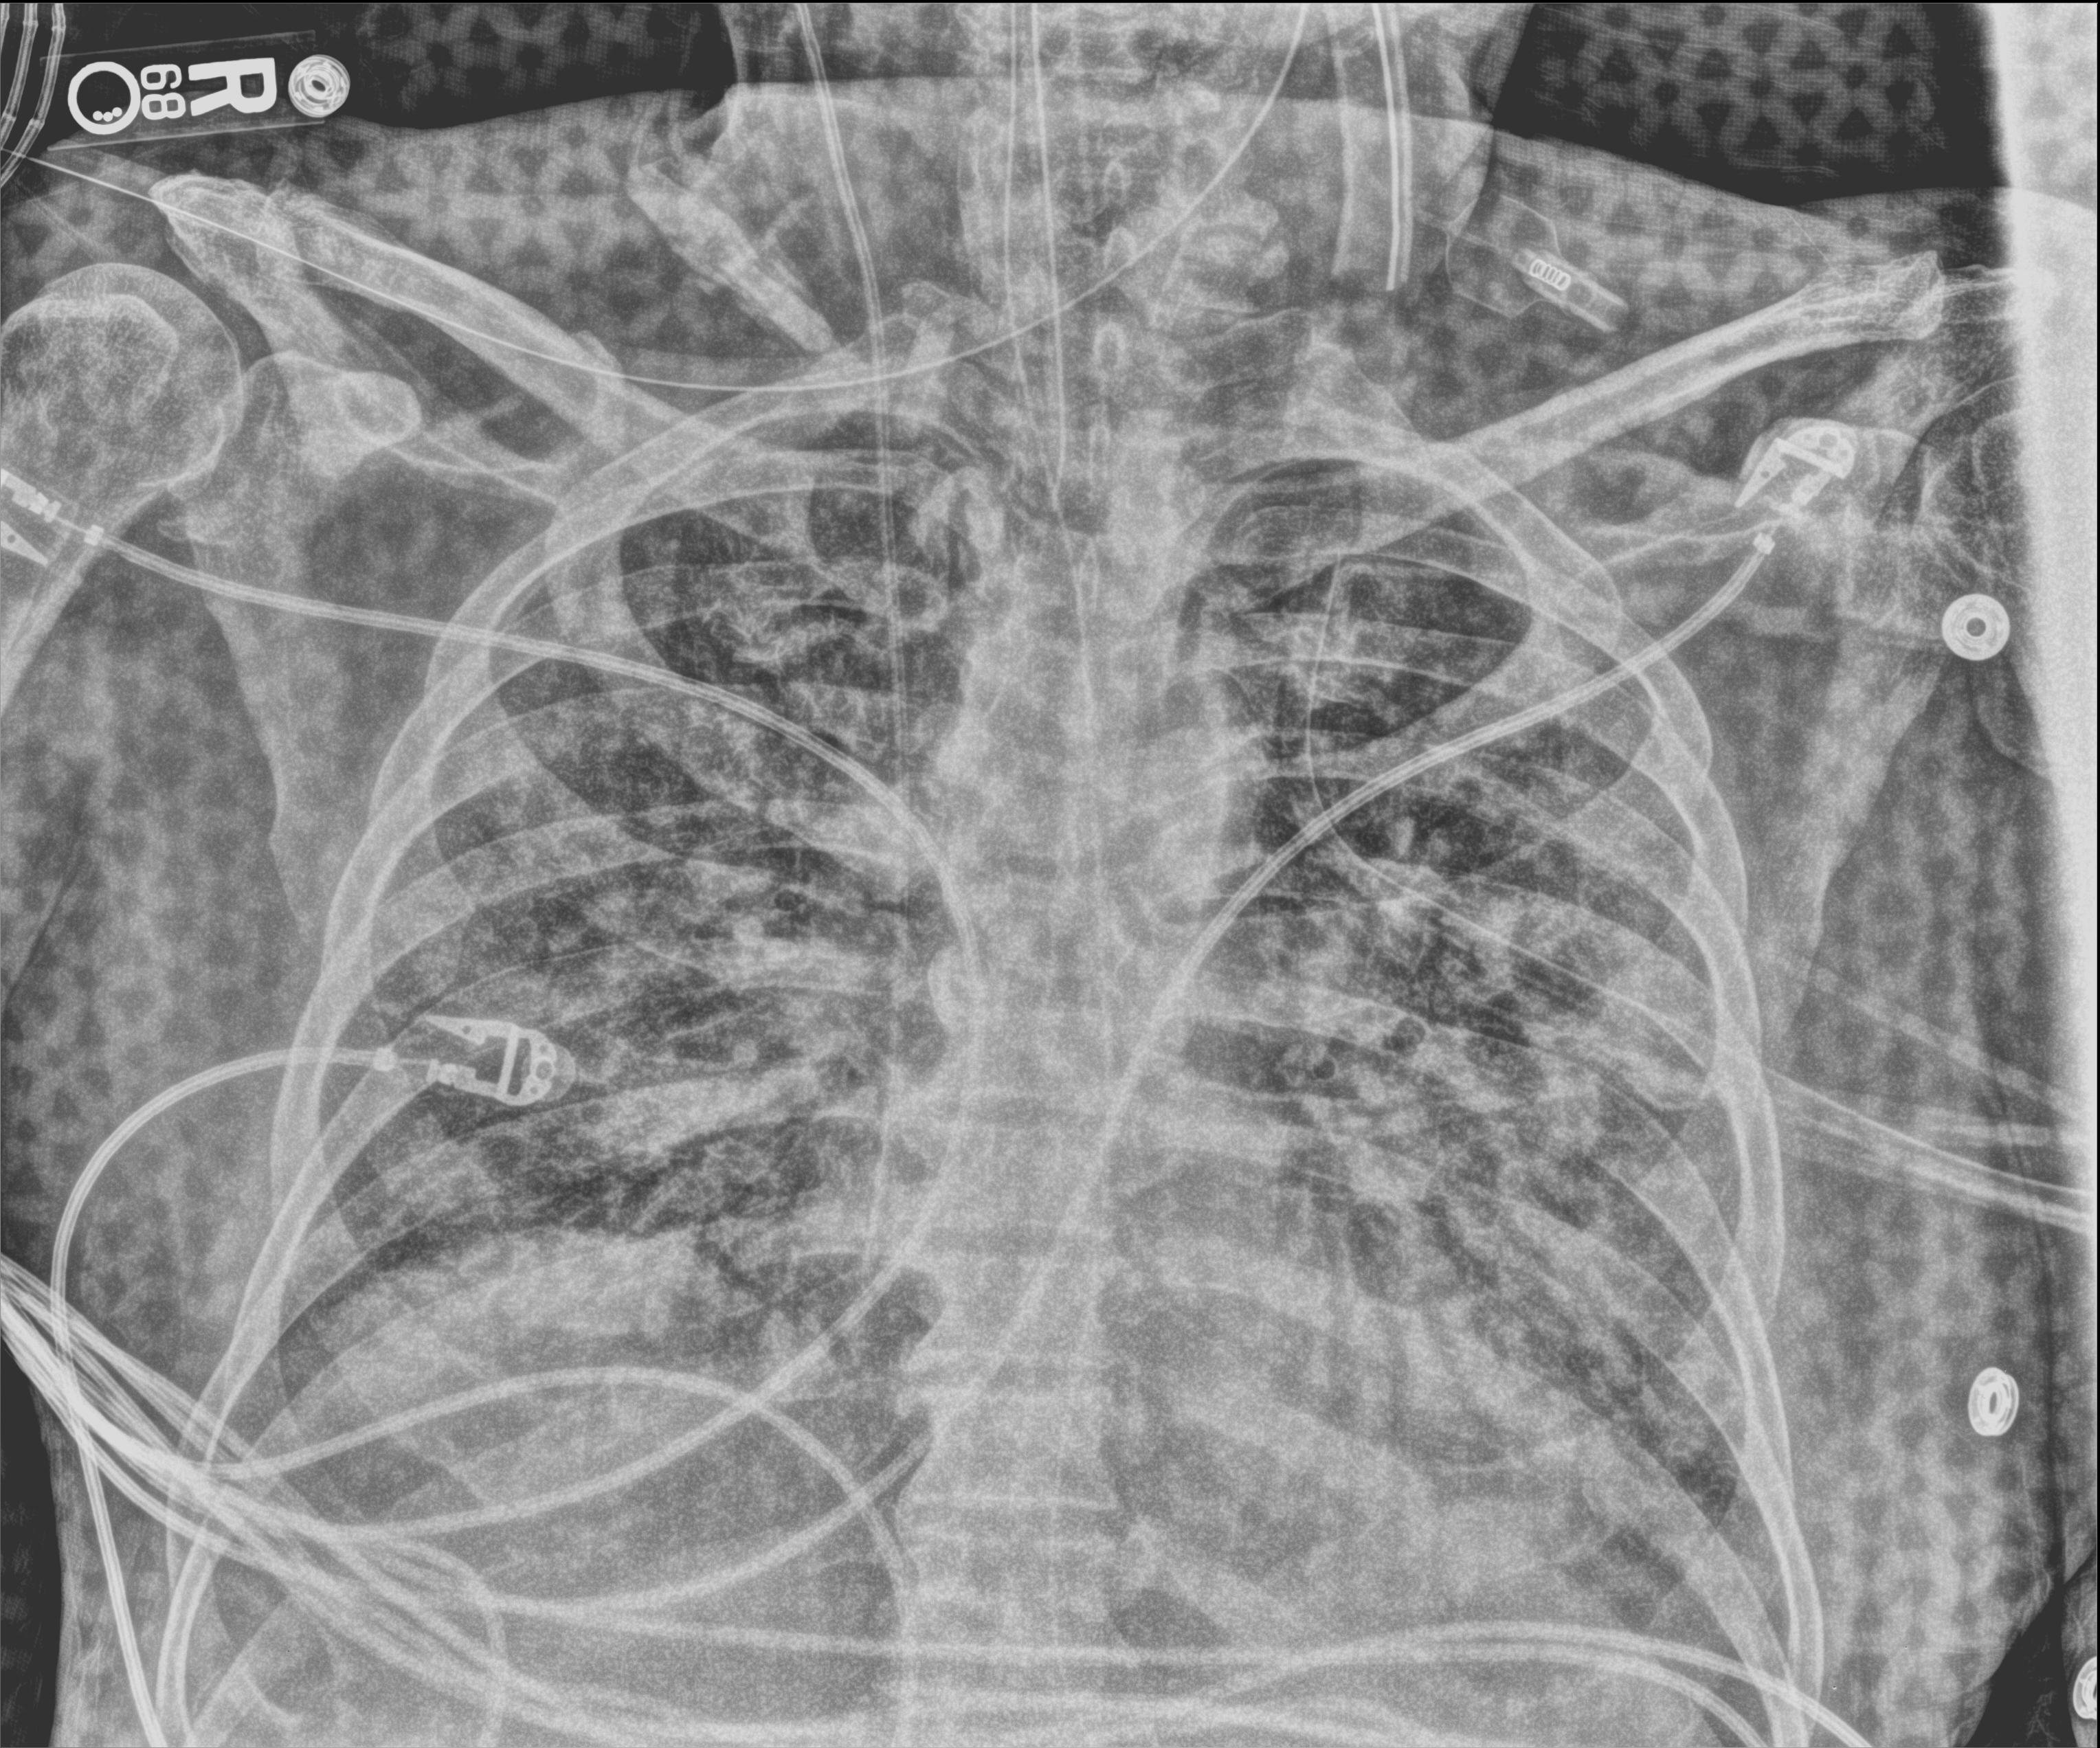
Bedside chest radiograph (computed radiography), anteroposterior (AP) projection. Male patient hospitalised with COVID-19, age 75–90 years.
Hospital-stay facts (about this admission, not read from this image; timing relative to this image not recorded):
- admitted to intensive care during this hospital stay: yes
- mechanically ventilated during this hospital stay: yes